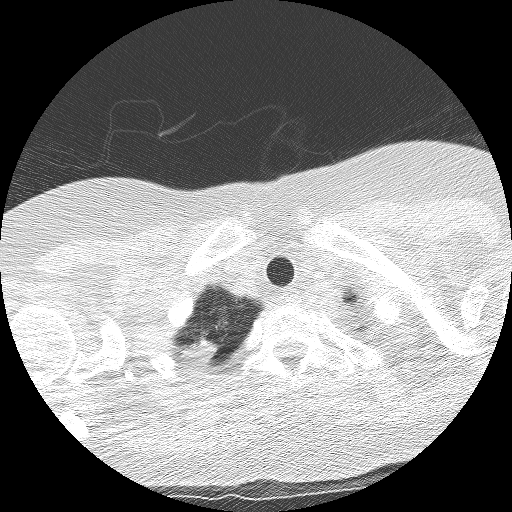
Chest CT (low-dose screening protocol), one axial image, third screening round (two years after baseline), lung window (W 1500 / L -600 HU), lung (sharp) reconstruction kernel (BONE), slice 9 of 130 in the series. Female, age 56 years at enrolment. Current smoker at enrolment.
- Lesion marked by an expert reader, bounding box (x1, y1, x2, y2) in pixels: (172, 326, 228, 372).
- Reader record for this screening exam (exam-level; its link to the box is not recorded): non-calcified nodule or mass ≥4 mm, right upper lobe, 17 × 10 mm, spiculated (stellate) margins, mixed attenuation, pre-existing on the prior screen: yes; interval growth: yes.